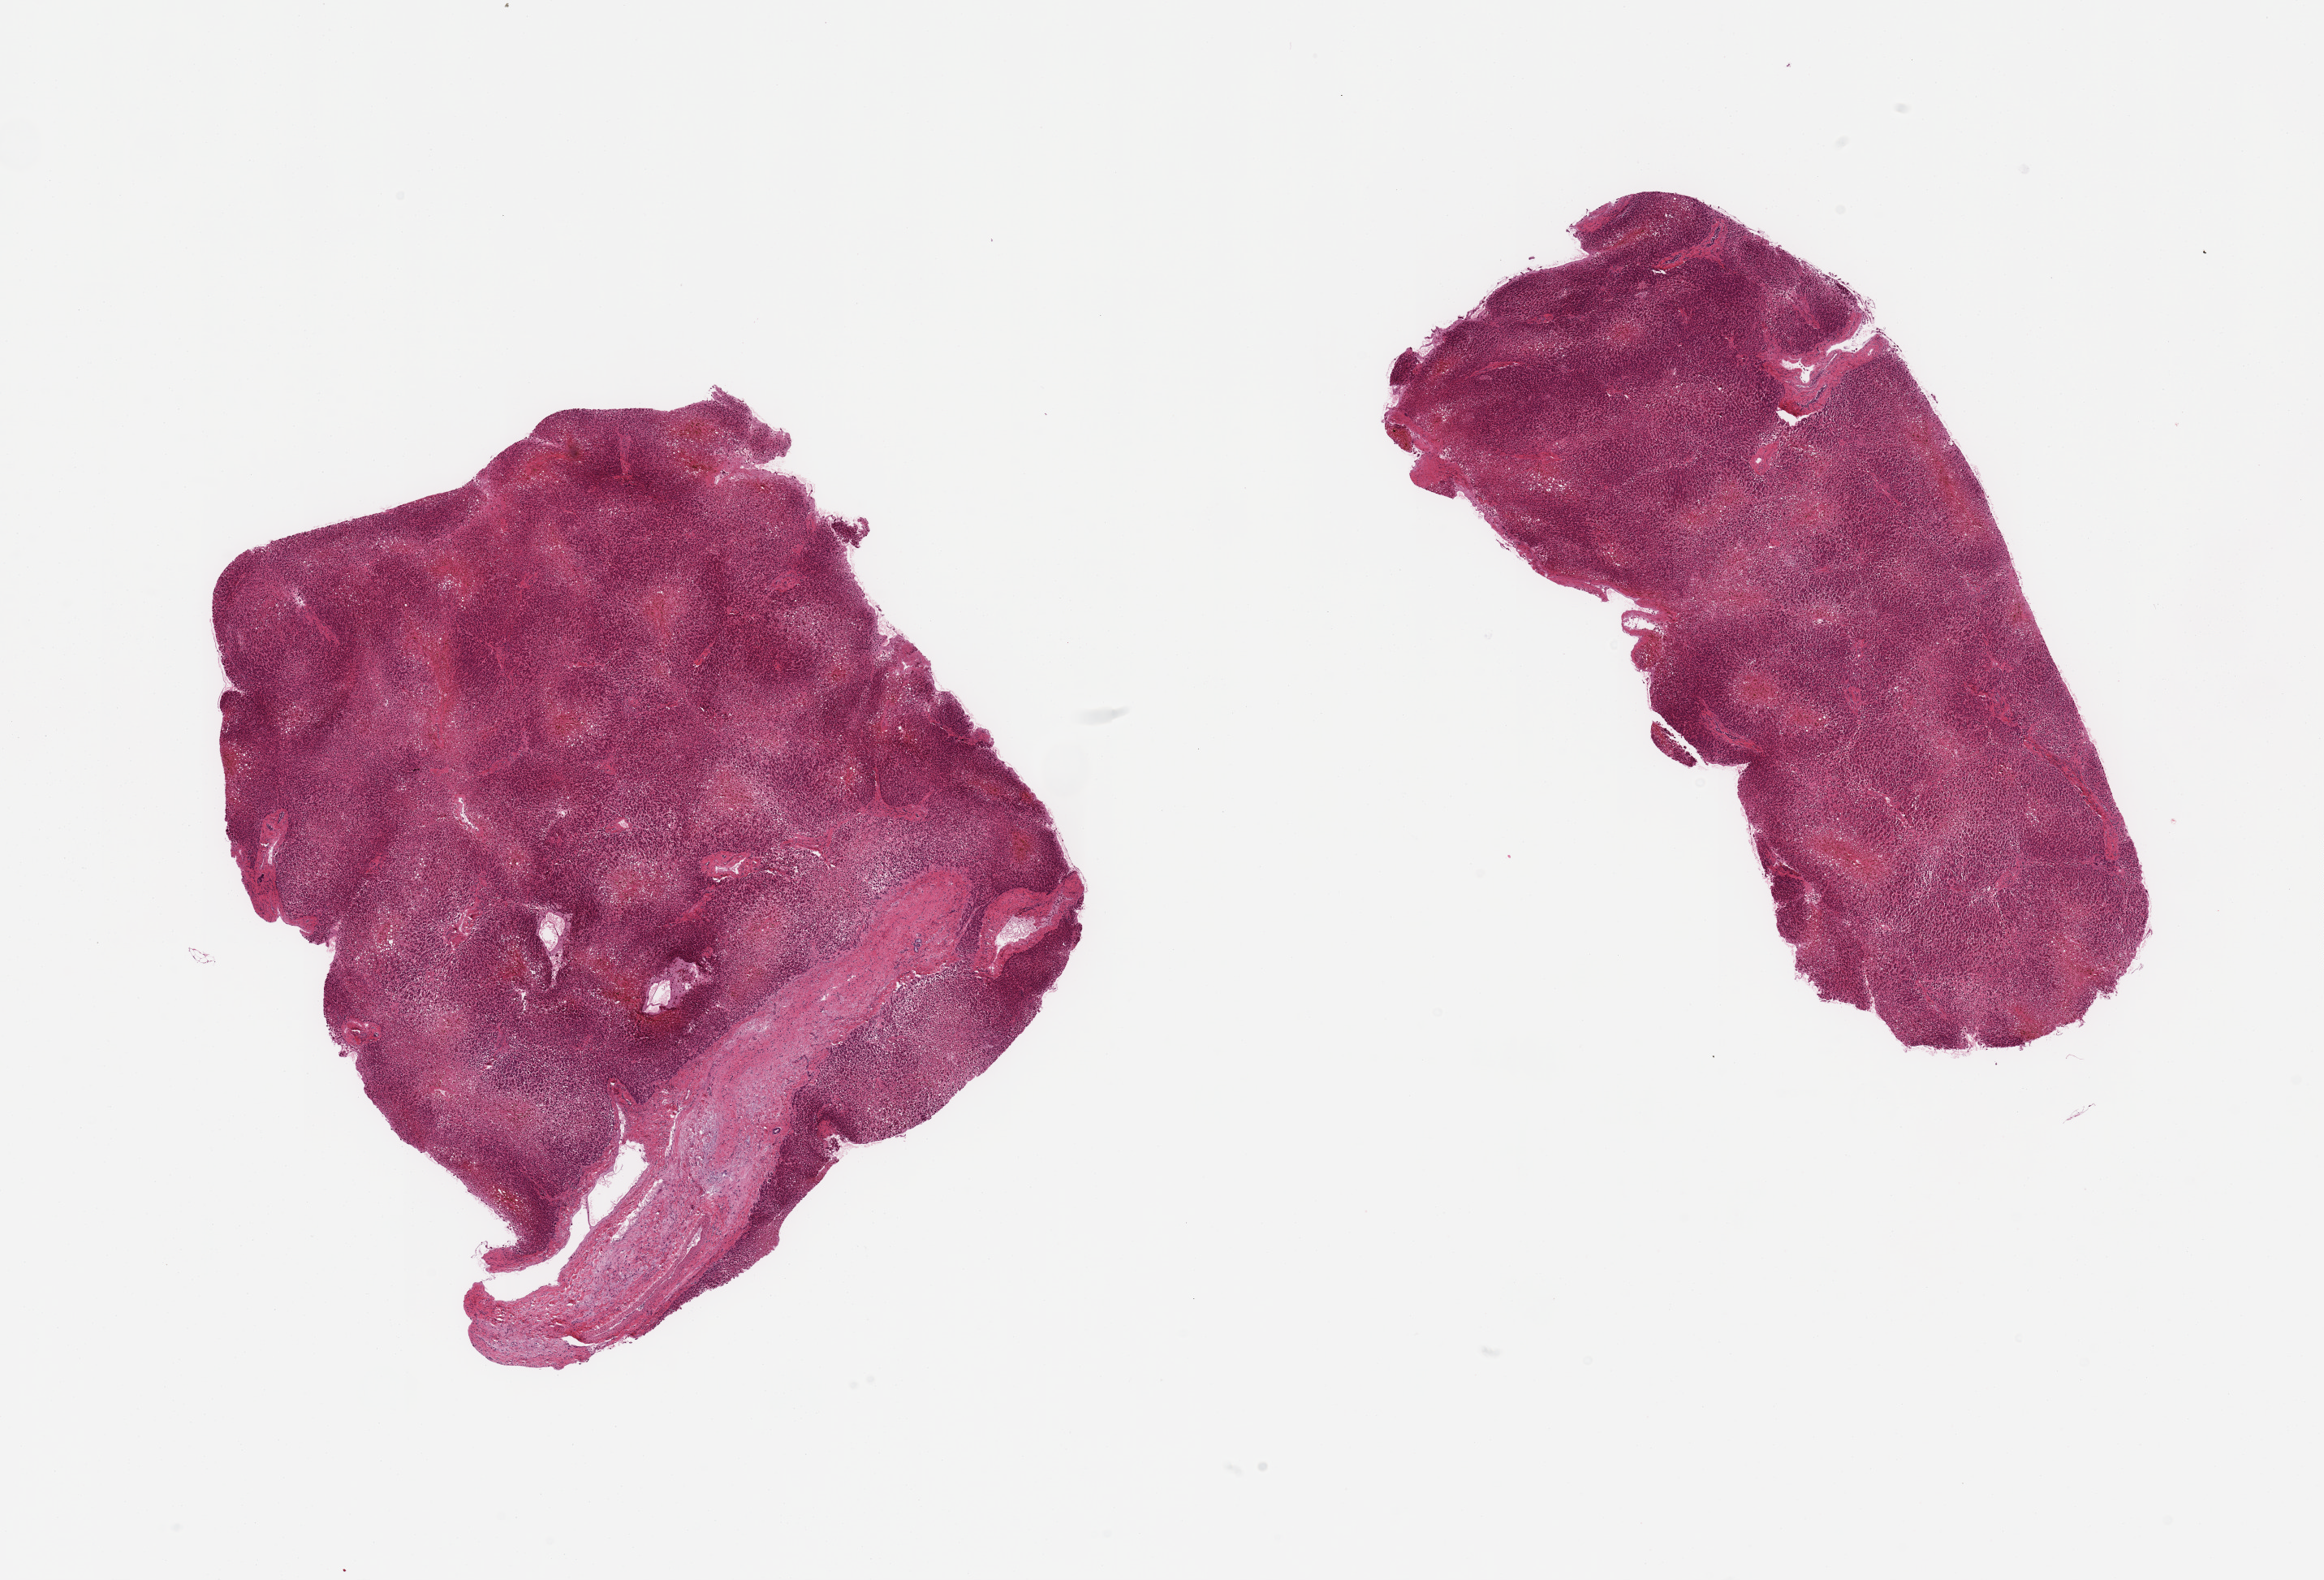
H&E whole-slide image, shown as a low-resolution overview of the whole scanned area (about 22.6 x 15.4 mm), PAXgene-fixed, paraffin-embedded tissue, target tissue: liver, tissue donor sample. Donor: male.
Reviewer comment on this tissue sample: 2 pieces, pronounced centrilobular necrosis, 40% of parenchyma, moderate macrovesciluar steatosis.